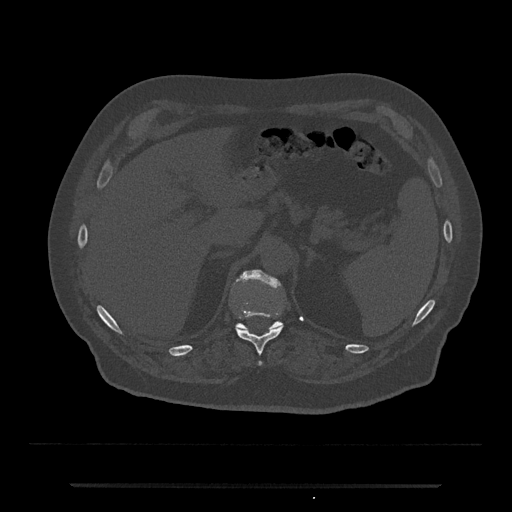
CT including the spine, one axial slice. Slice 633 of 797 in the series (ordered by position). Reconstruction kernel Br40s/3. 120 kVp. Bone window (W 1800 / L 400 HU). 512 × 512 image matrix, field of view 434 × 434 mm. Male patient, age 80 years. From the clinical record (not read from this slice): primary cancer: prostate.
Annotated regions visible in this slice (semi-automatic segmentation, software-assisted and operator-edited):
- T11 vertebra: box from (x=236, y=312) to (x=282, y=366) px
- T12 vertebra: (x=235, y=269)–(x=283, y=331)